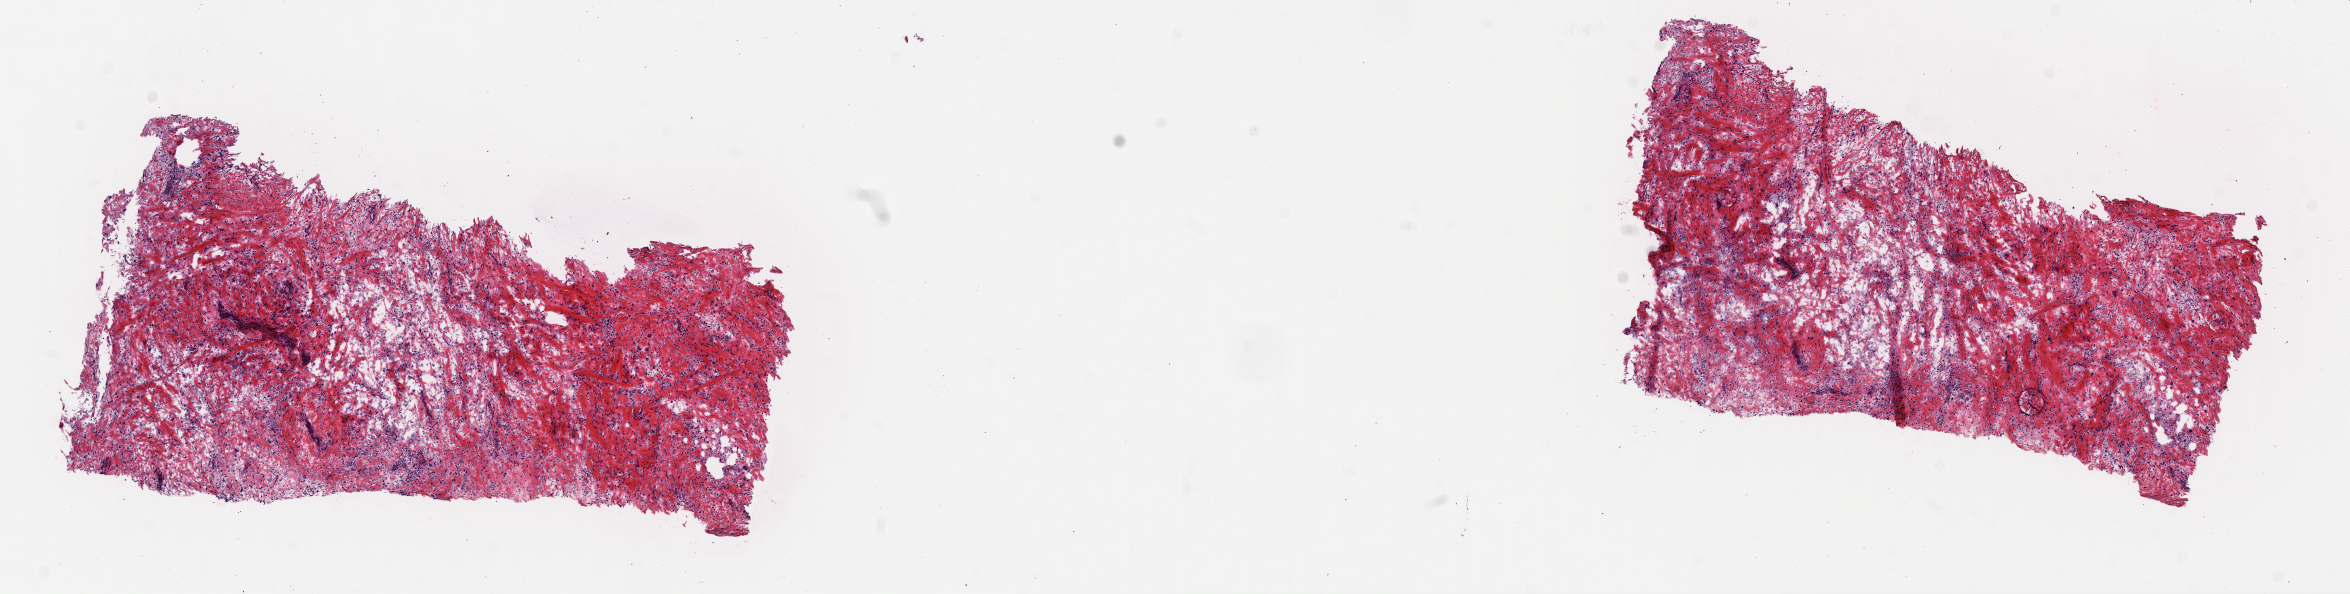
Hematoxylin and eosin (H&E) stained whole-slide image, shown as a low-resolution overview of the whole scanned area (about 18.6 x 4.7 mm, slide scanned at 40x); frozen section from the top of the tissue portion; sample: primary tumour, retroperitoneum and peritoneum. Male patient; age at initial diagnosis 60 years. Composition of this section per pathologist review: tumour cells 75%, tumour nuclei 97%, normal cells 0%, stromal cells 25%, necrosis 0%. Inflammatory infiltration, as recorded: lymphocyte infiltration 1%, monocyte infiltration 2%, neutrophil infiltration 0%.
Pathologic diagnosis: Dedifferentiated liposarcoma (retroperitoneum).